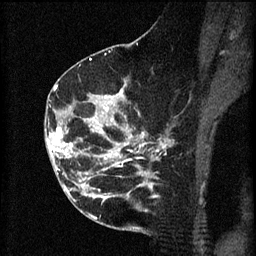
Breast MRI (dynamic contrast-enhanced), one sagittal slice. Slice 31 of 60 in the series (ordered by position). 3 images stored at this slice position (order not interpretable as contrast timing). 1.5 T. TE 4.2 ms, TR 8.2 ms. 256 × 256 image matrix, field of view 180 × 180 mm. Female patient, age 49 years.
Structures marked on this image (semi-automatically segmented with operator editing):
- analysis volume of interest (the breast-tissue region the enhancement analysis was run in; not a lesion): bounding box (x1, y1, x2, y2) in pixels: (45, 126, 105, 177)
- tumour enhancement mask (voxels above the 70 % enhancement threshold inside the analysis volume of interest): (47, 126, 105, 159)